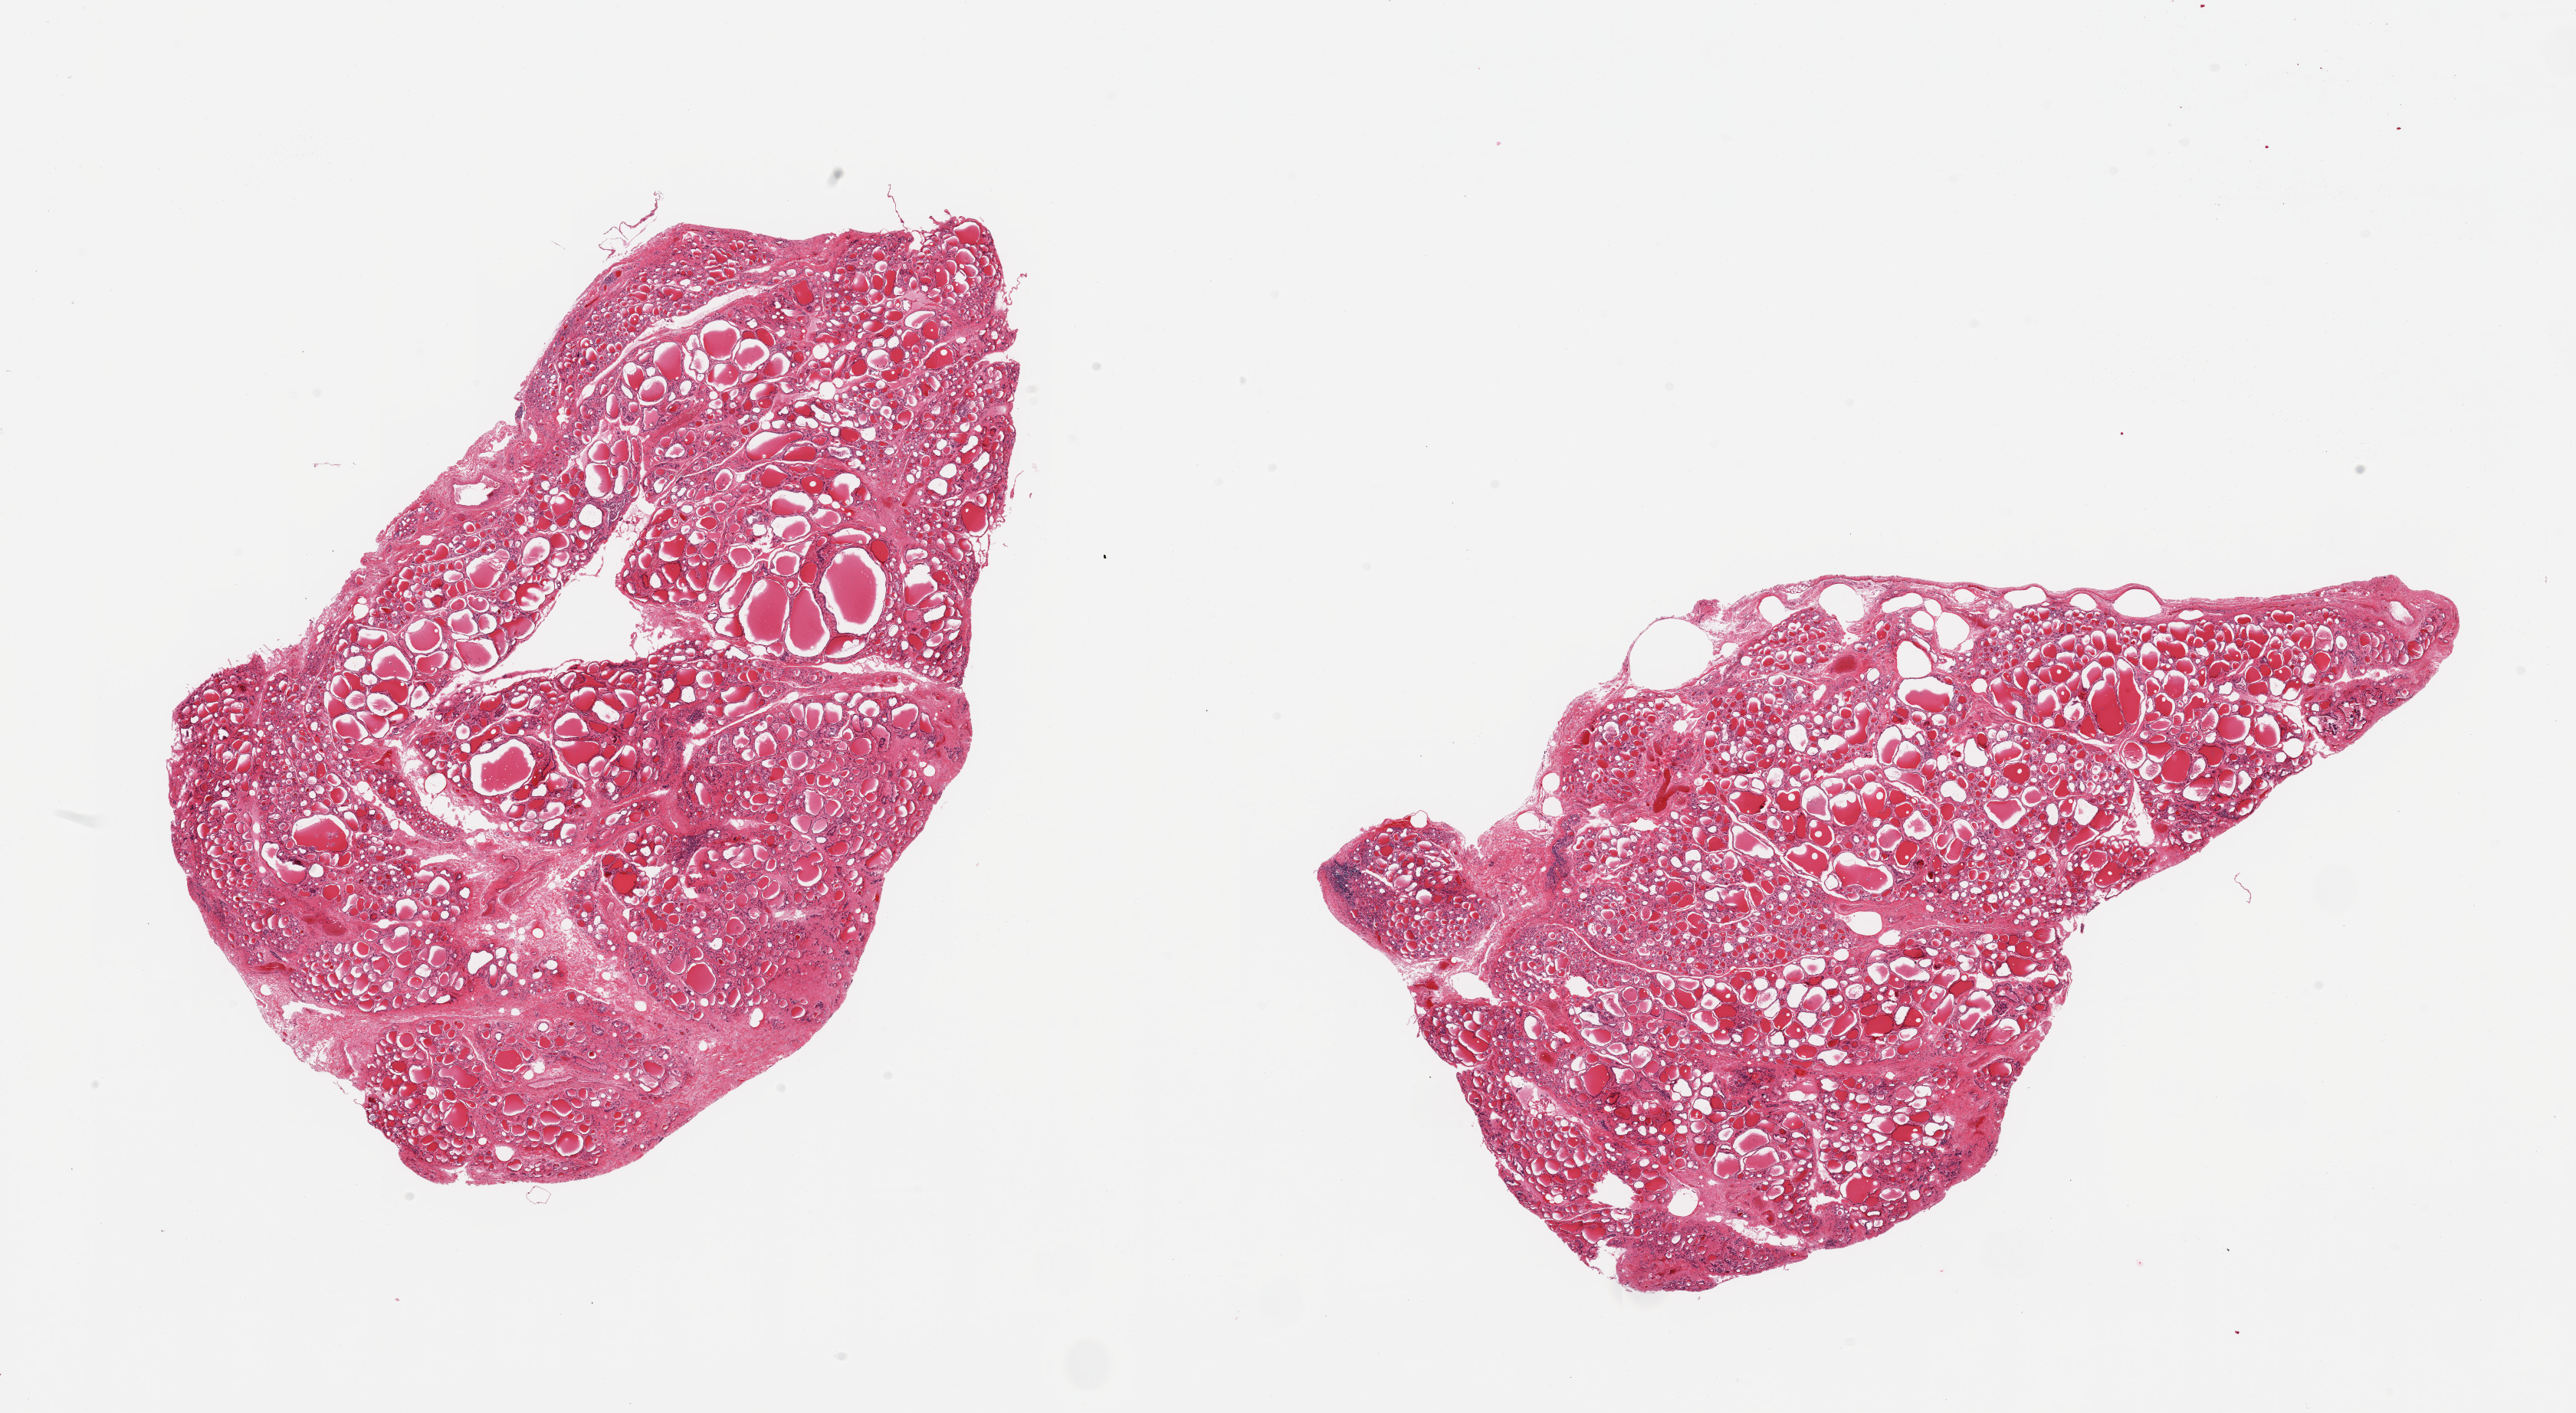
Whole-slide image, H&E stain, brightfield — whole scanned area (about 26.6 x 14.6 mm, acquisition: 20x scan) shown as a low-resolution overview, PAXgene-fixed paraffin-embedded (PFPE) section, sampled site (target tissue): thyroid, tissue donor sample. Male donor.
Reviewer comment on this tissue sample: 2 pieces; interstitial fibrosis with nodularity; rare lymphocytic aggregates; congestion.